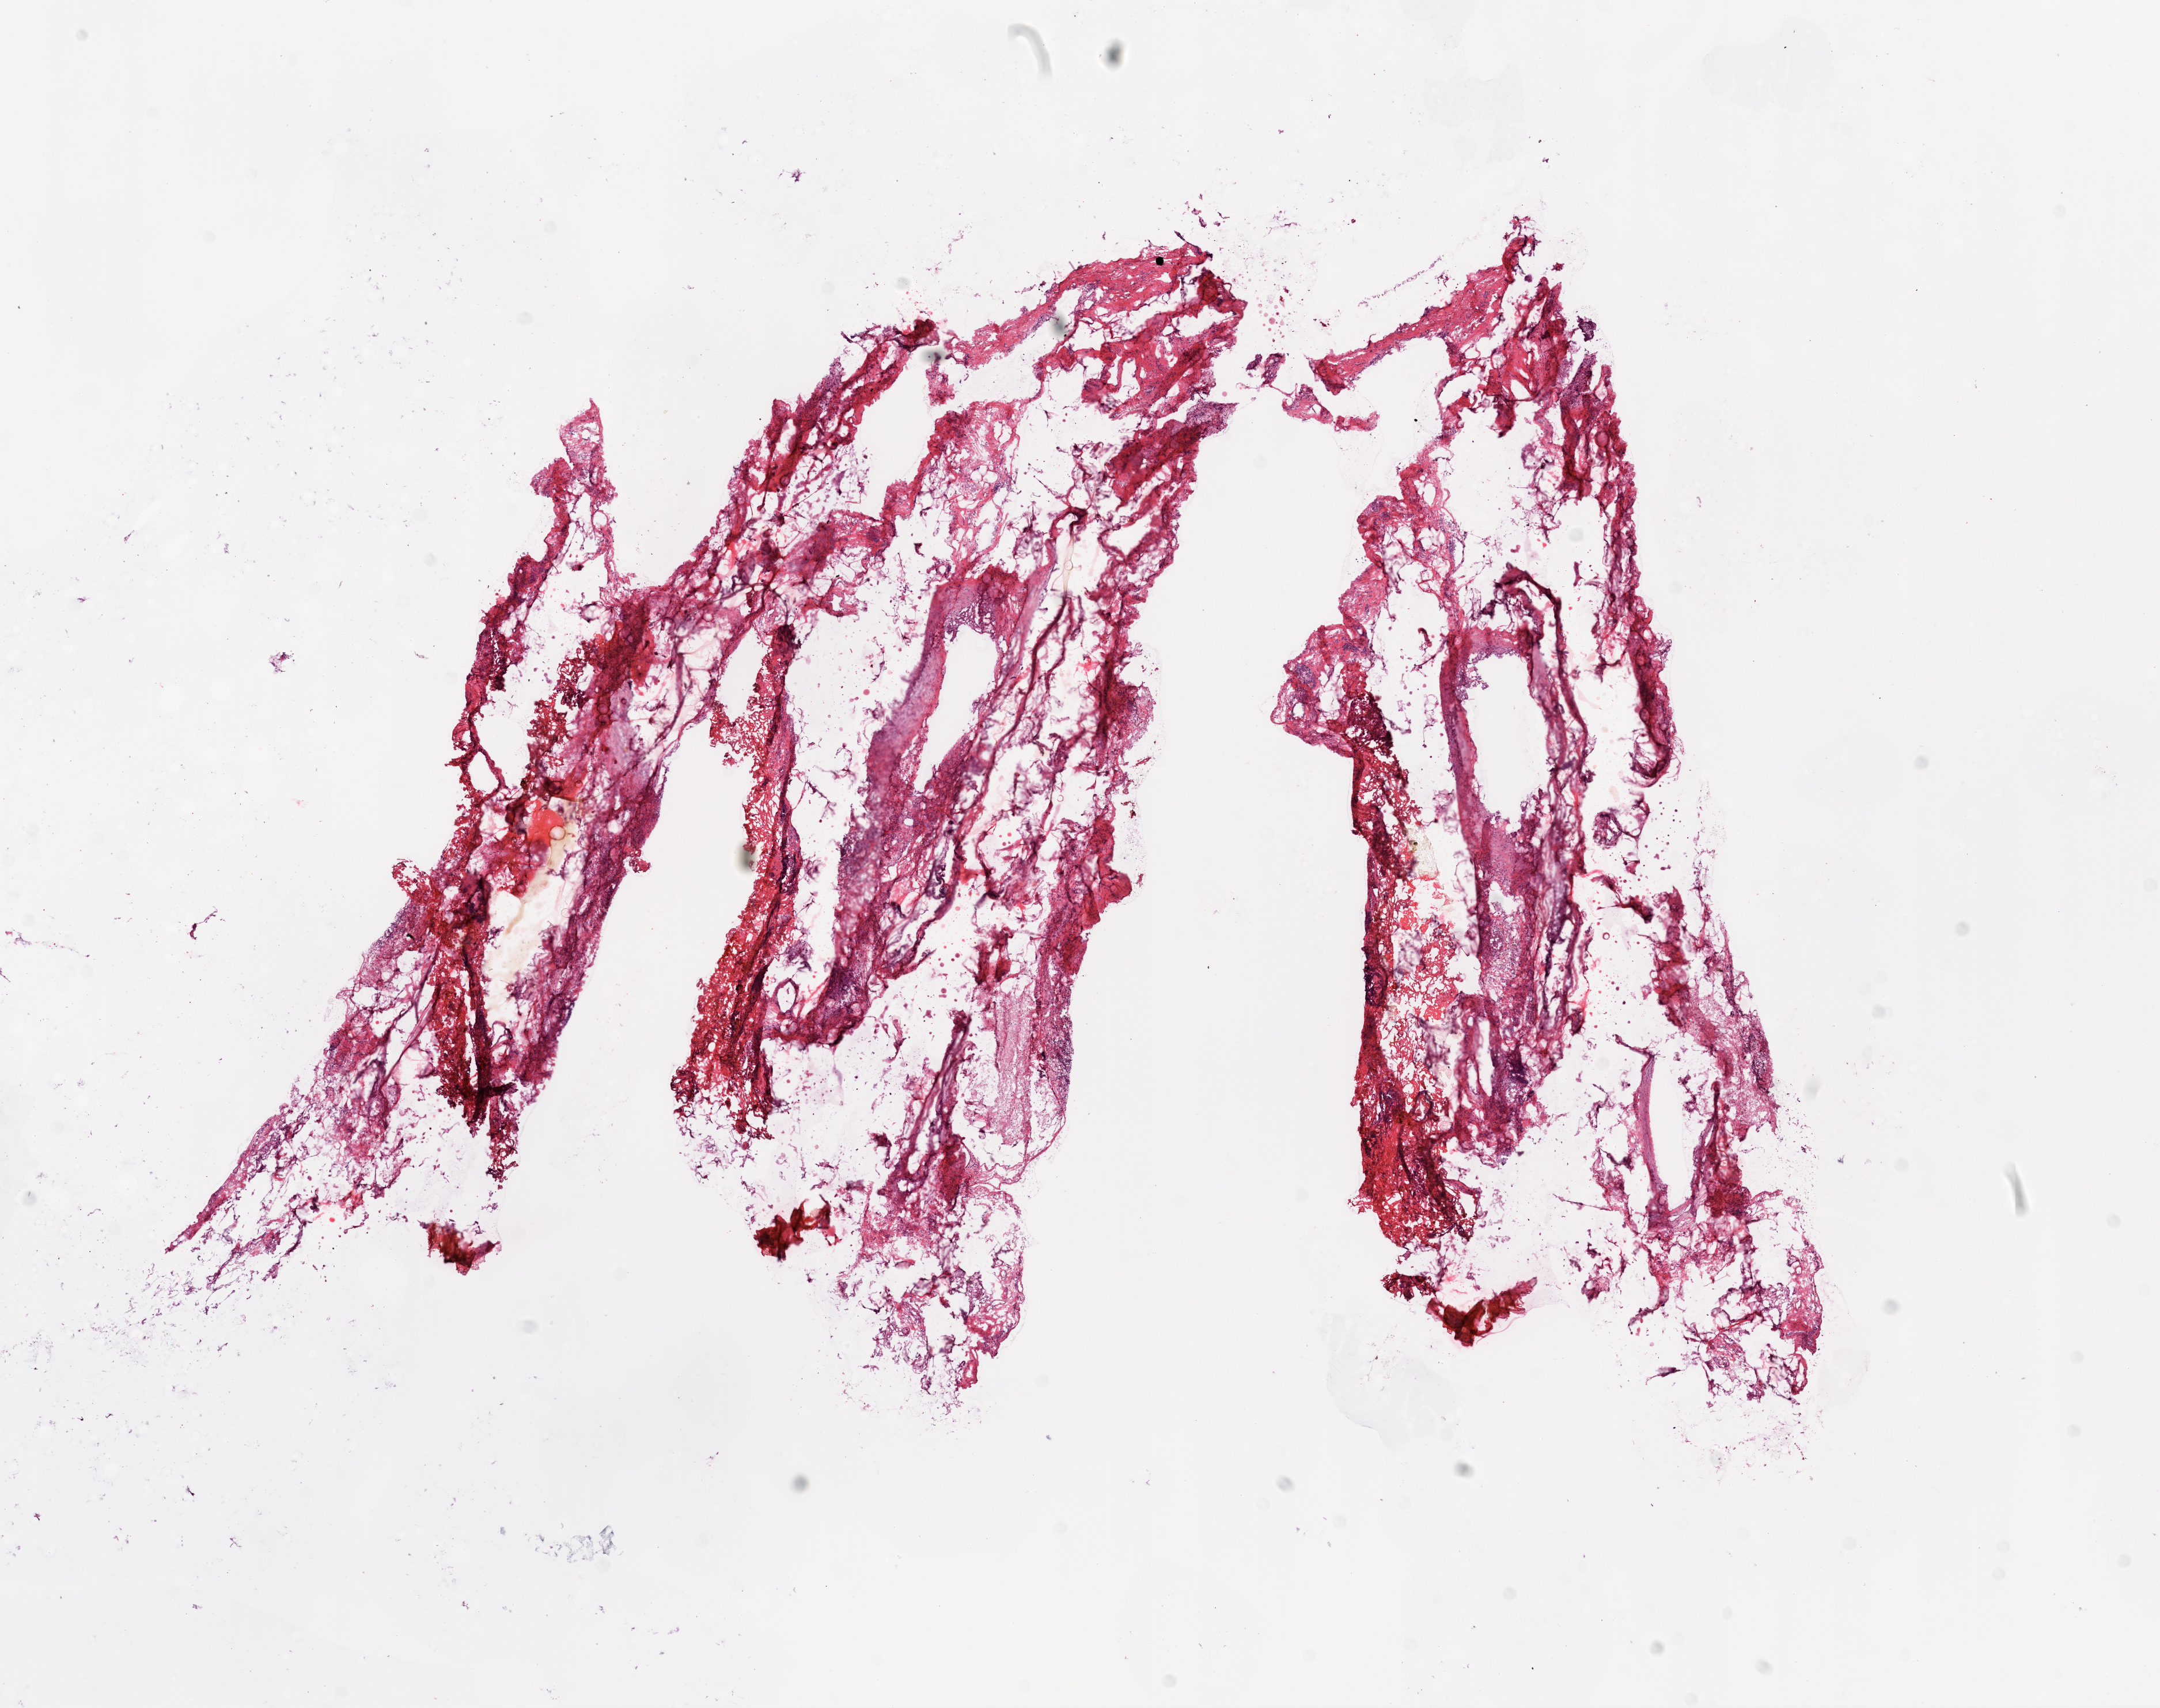
Digitized H&E-stained tissue section (whole slide), whole scanned area (about 15.0 x 11.9 mm, acquisition: 20x scan) shown as a low-resolution overview. Frozen section from the top of the tissue portion. Sample: solid tissue normal (non-tumour tissue), ovary. Female, age 60 years at initial diagnosis.
This section: solid tissue normal (non-tumour) sample from the same patient. Patient diagnosis: Serous cystadenocarcinoma, NOS.